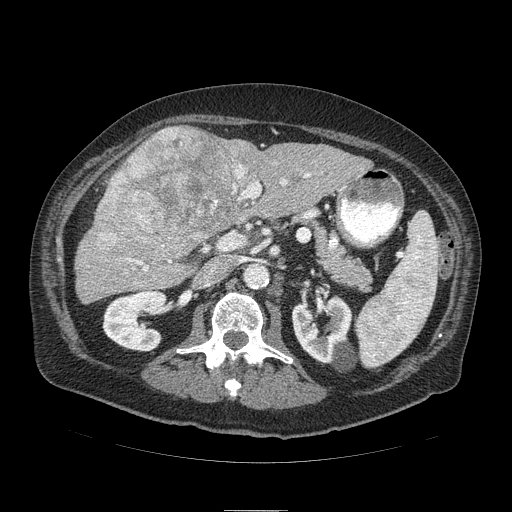
Contrast-enhanced abdominal CT (liver protocol), one axial slice. Position 42 of 103 along the scan axis. Reconstruction kernel STANDARD. 120 kVp. Soft-tissue window (W 400 / L 40 HU). 2.5 mm slice thickness. 512 × 512 image matrix, field of view 440 × 440 mm. Case-level facts recorded for this patient, not image findings: diagnosis: hepatocellular carcinoma (patient treated with transarterial chemoembolisation; whether this scan precedes or follows treatment is not stated here); TNM stage (as recorded): Stage-IIIA; Child-Pugh class: B; tumour nodularity: multinodular; tumour size: 13 cm.
Structures marked on this image (semi-automatic segmentation, software-assisted and operator-edited):
- liver parenchyma outside the tumour (the mass and vessels are separate outlines, so this box may not span the whole liver): box from (x=74, y=134) to (x=371, y=302) px
- mass: (x=90, y=126)–(x=257, y=262)
- liver vessels: (x=127, y=174)–(x=310, y=270)